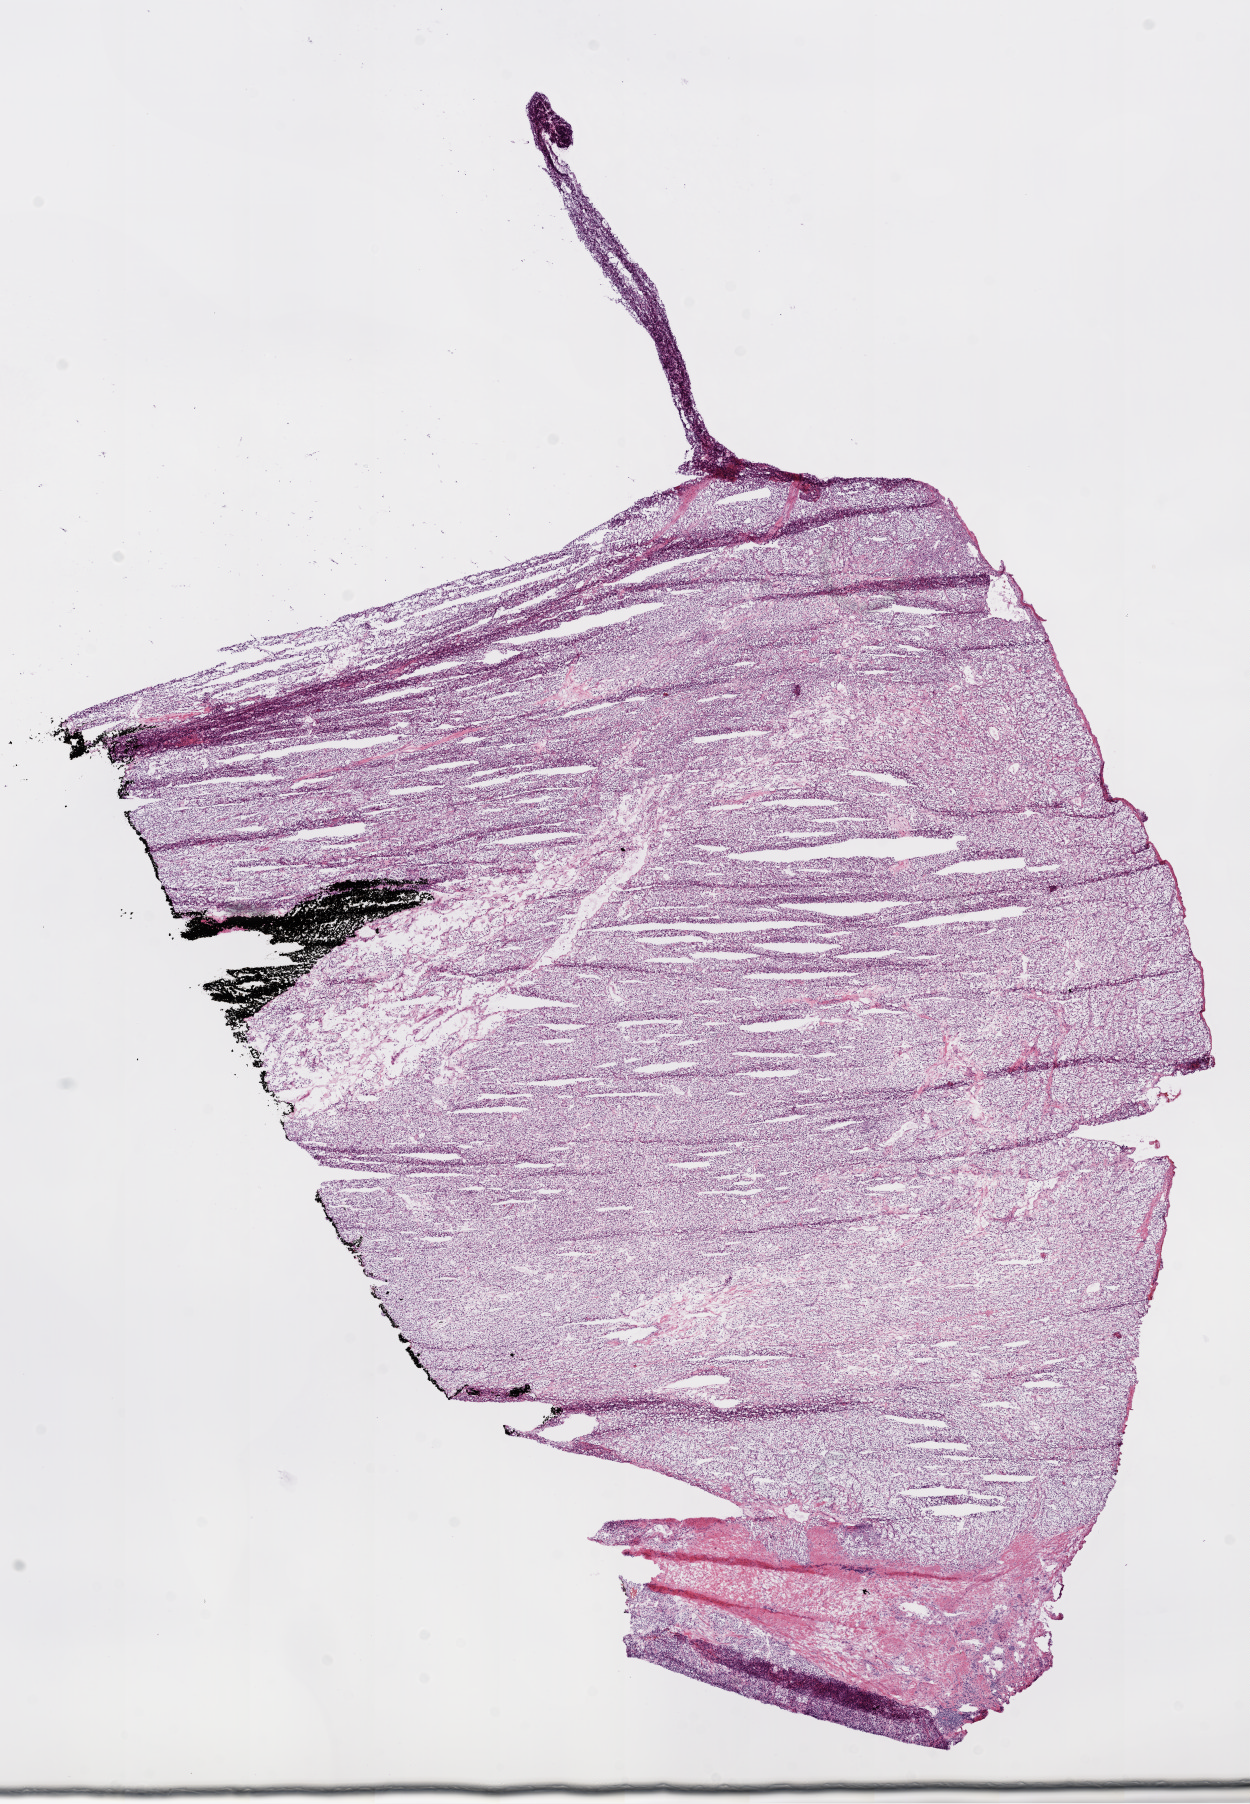
Whole-slide histology image, H&E-stained — whole scanned area (about 10.0 x 14.5 mm, from a 20x scan) shown as a low-resolution overview; frozen section from the bottom of the tissue portion; sample: primary tumour, kidney. Female, age 52 years at initial diagnosis. Histologic grade: G1 (well differentiated). Composition of this section per pathologist review: tumour cells 90%, tumour nuclei 90%, normal cells 0%, stromal cells 10%, necrosis 0%.
AJCC pathologic stage: I. Pathologic diagnosis: Clear cell adenocarcinoma, NOS.